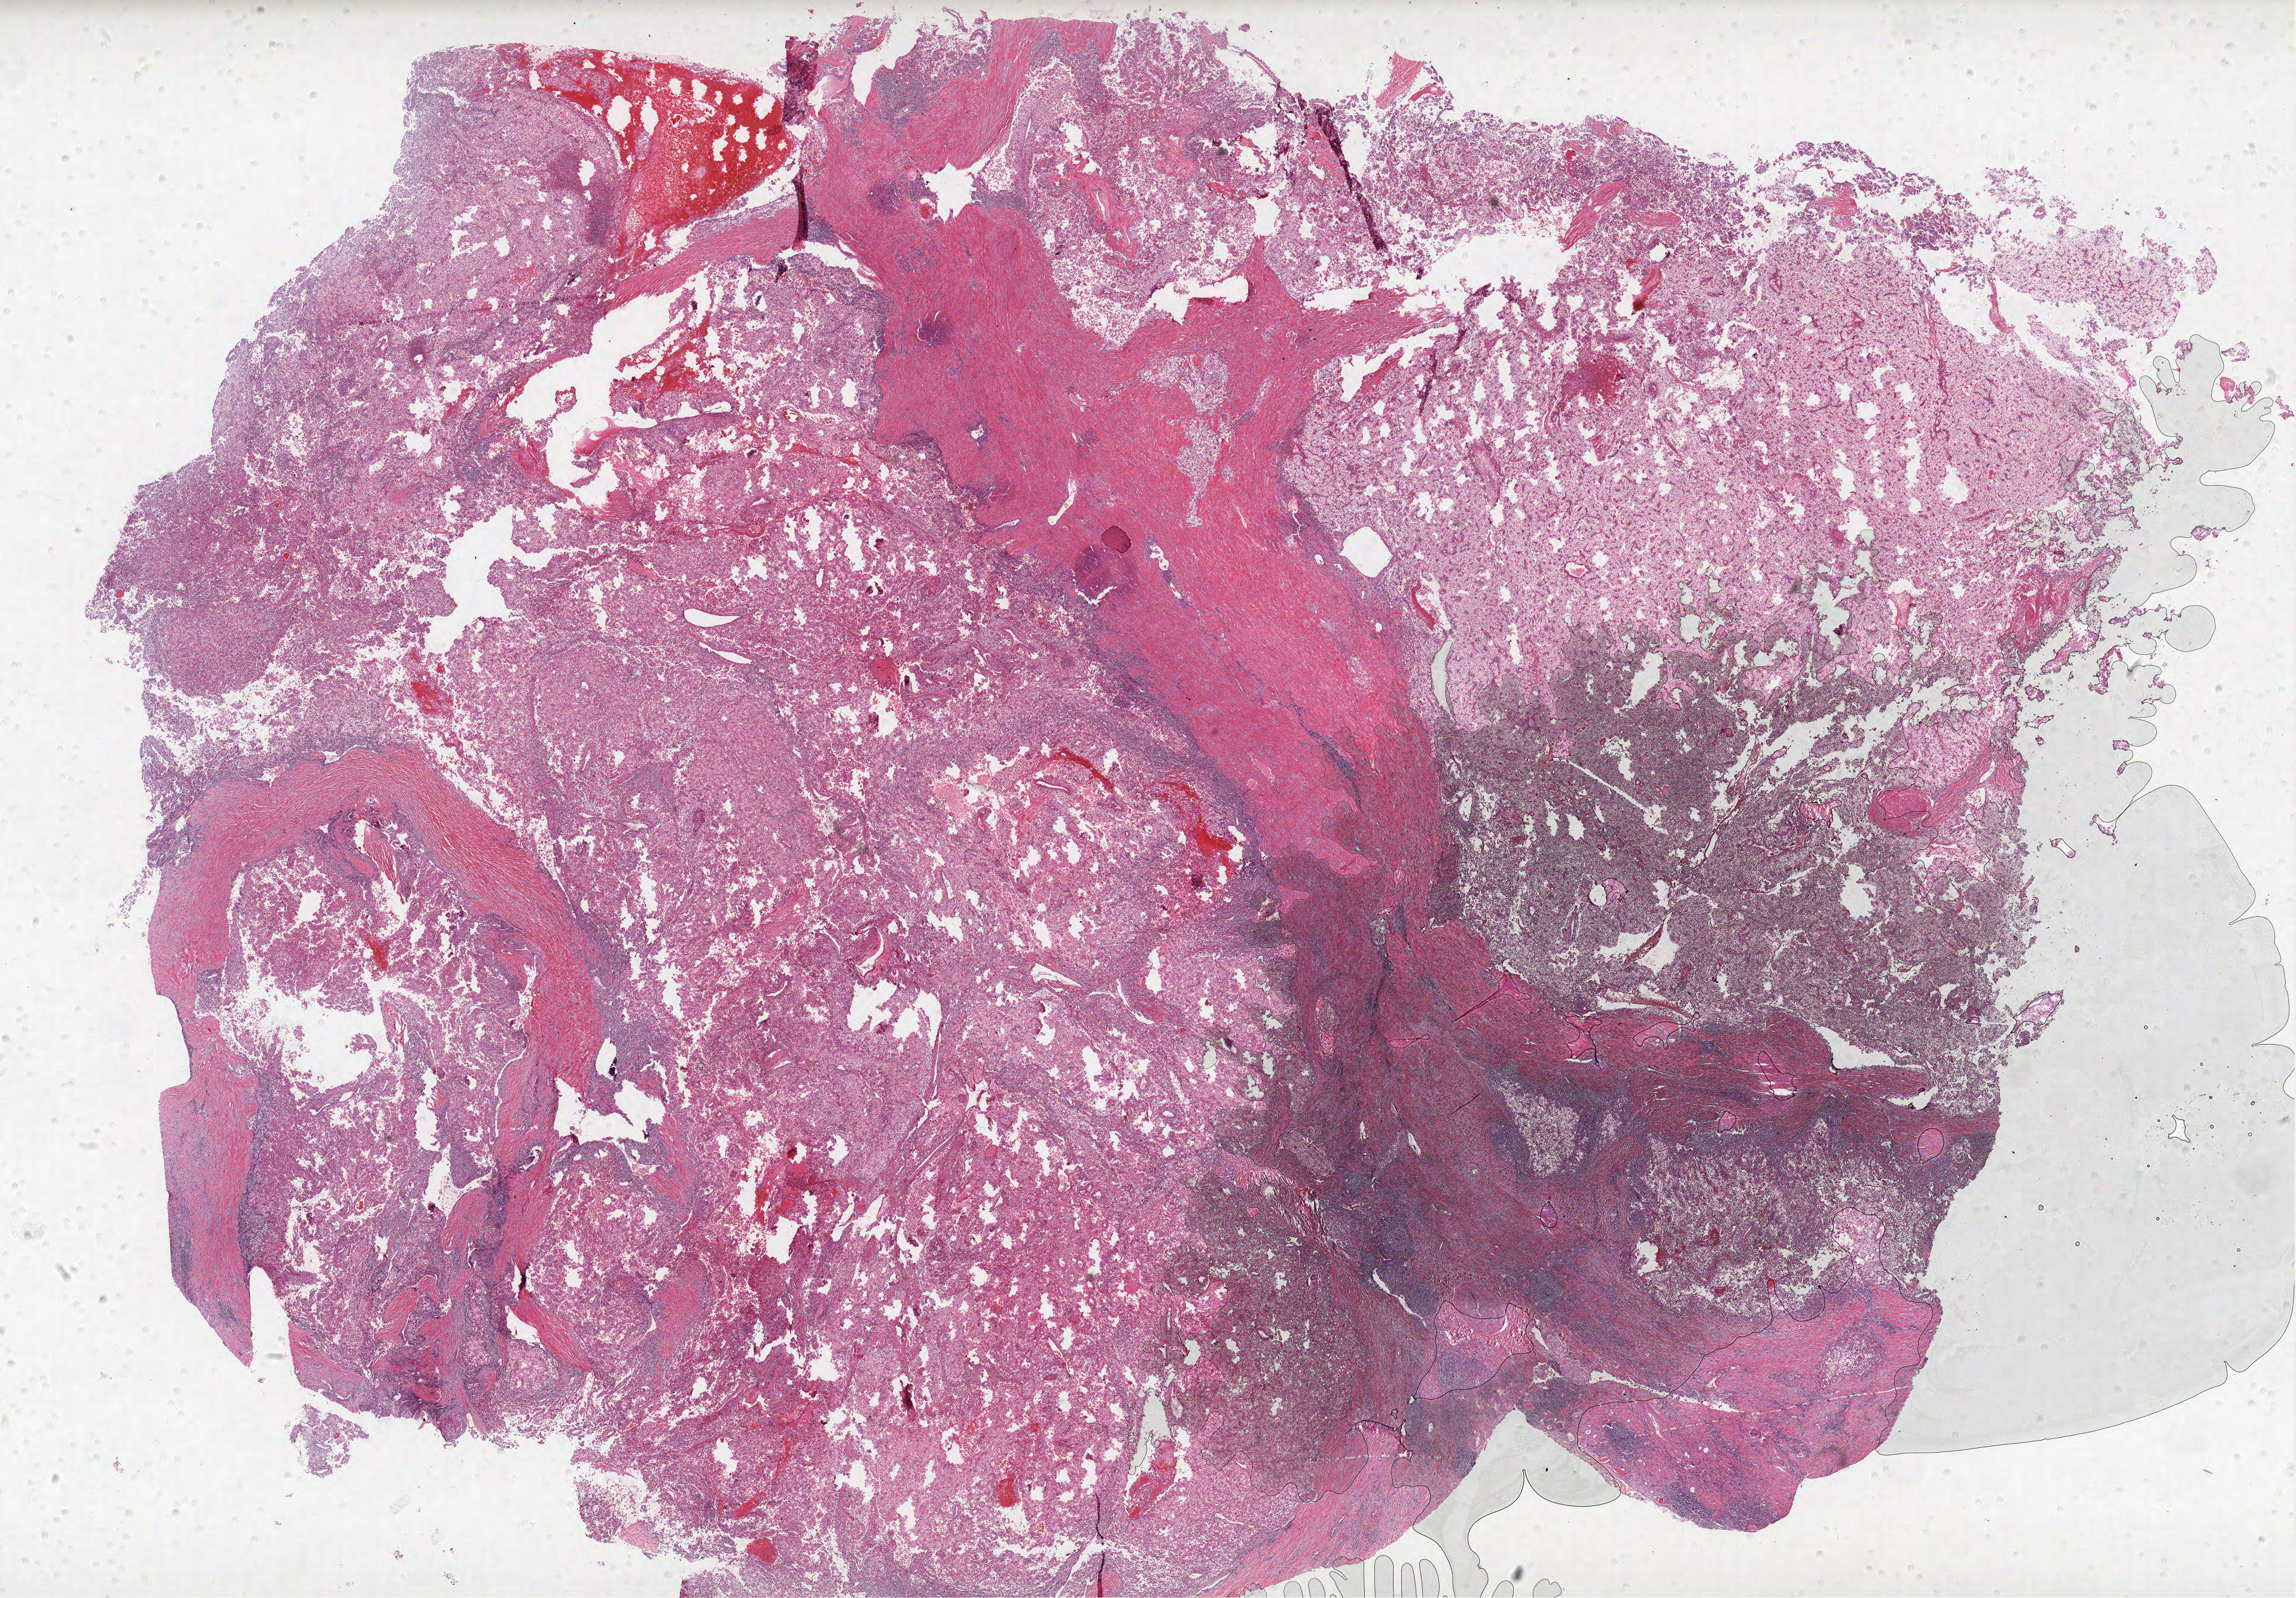
H&E whole-slide image — shown as a low-resolution overview of the whole scanned area (about 30.7 x 21.4 mm). Formalin-fixed paraffin-embedded (FFPE) diagnostic section. Sample: primary tumour, kidney. Patient: male, age at initial diagnosis 70 years. Histologic grade: G4 (undifferentiated).
AJCC pathologic stage: I. Lymph nodes positive (case pathology): 0 of 9 examined. Laterality: left. Diagnosis: Clear cell adenocarcinoma, NOS.